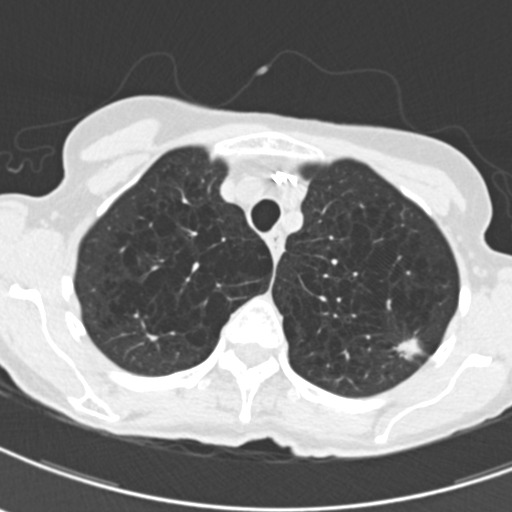
Low-dose screening chest CT, one axial slice; slice 161 of 203 in the series (ordered by position); 120 kVp; lung window (W 1500 / L -600 HU); 2 mm slice thickness; 512 × 512 image matrix, field of view 279 × 279 mm.
Structures marked on this image (outlined manually by an expert reader):
- lesion 1 (tumor, upper lobe of left lung): bounding box <394,337,421,359> (left, top, right, bottom; pixels)